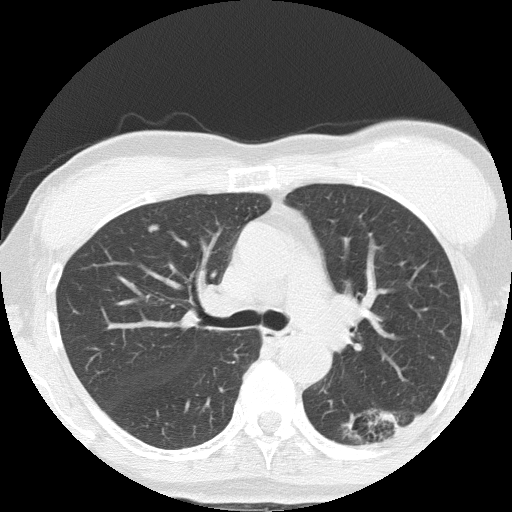
Chest CT (low-dose screening protocol), one axial image. Third screening round (two years after baseline). Lung window (W 1500 / L -600 HU). 2 mm slice thickness. Slice 57 of 152 in the series. 512 × 512 image matrix, field of view 308 × 308 mm. Female, age 64 years at enrolment. Former smoker at enrolment.
- Lesion marked by an expert reader, bounding box [x1, y1, x2, y2] px = [345, 387, 431, 455].
- The screening reader recorded 3 non-calcified nodules or masses ≥4 mm on this exam (right upper lobe, left lower lobe, right middle lobe); which of them this box marks is not recorded.
- Official screen result: positive, other.
- Later outcome: lung cancer diagnosed 212 days after this screen — adenocarcinoma, NOS, left lower lobe, moderately differentiated (G2), stage IA (AJCC 6th edition), 17 mm at pathology.